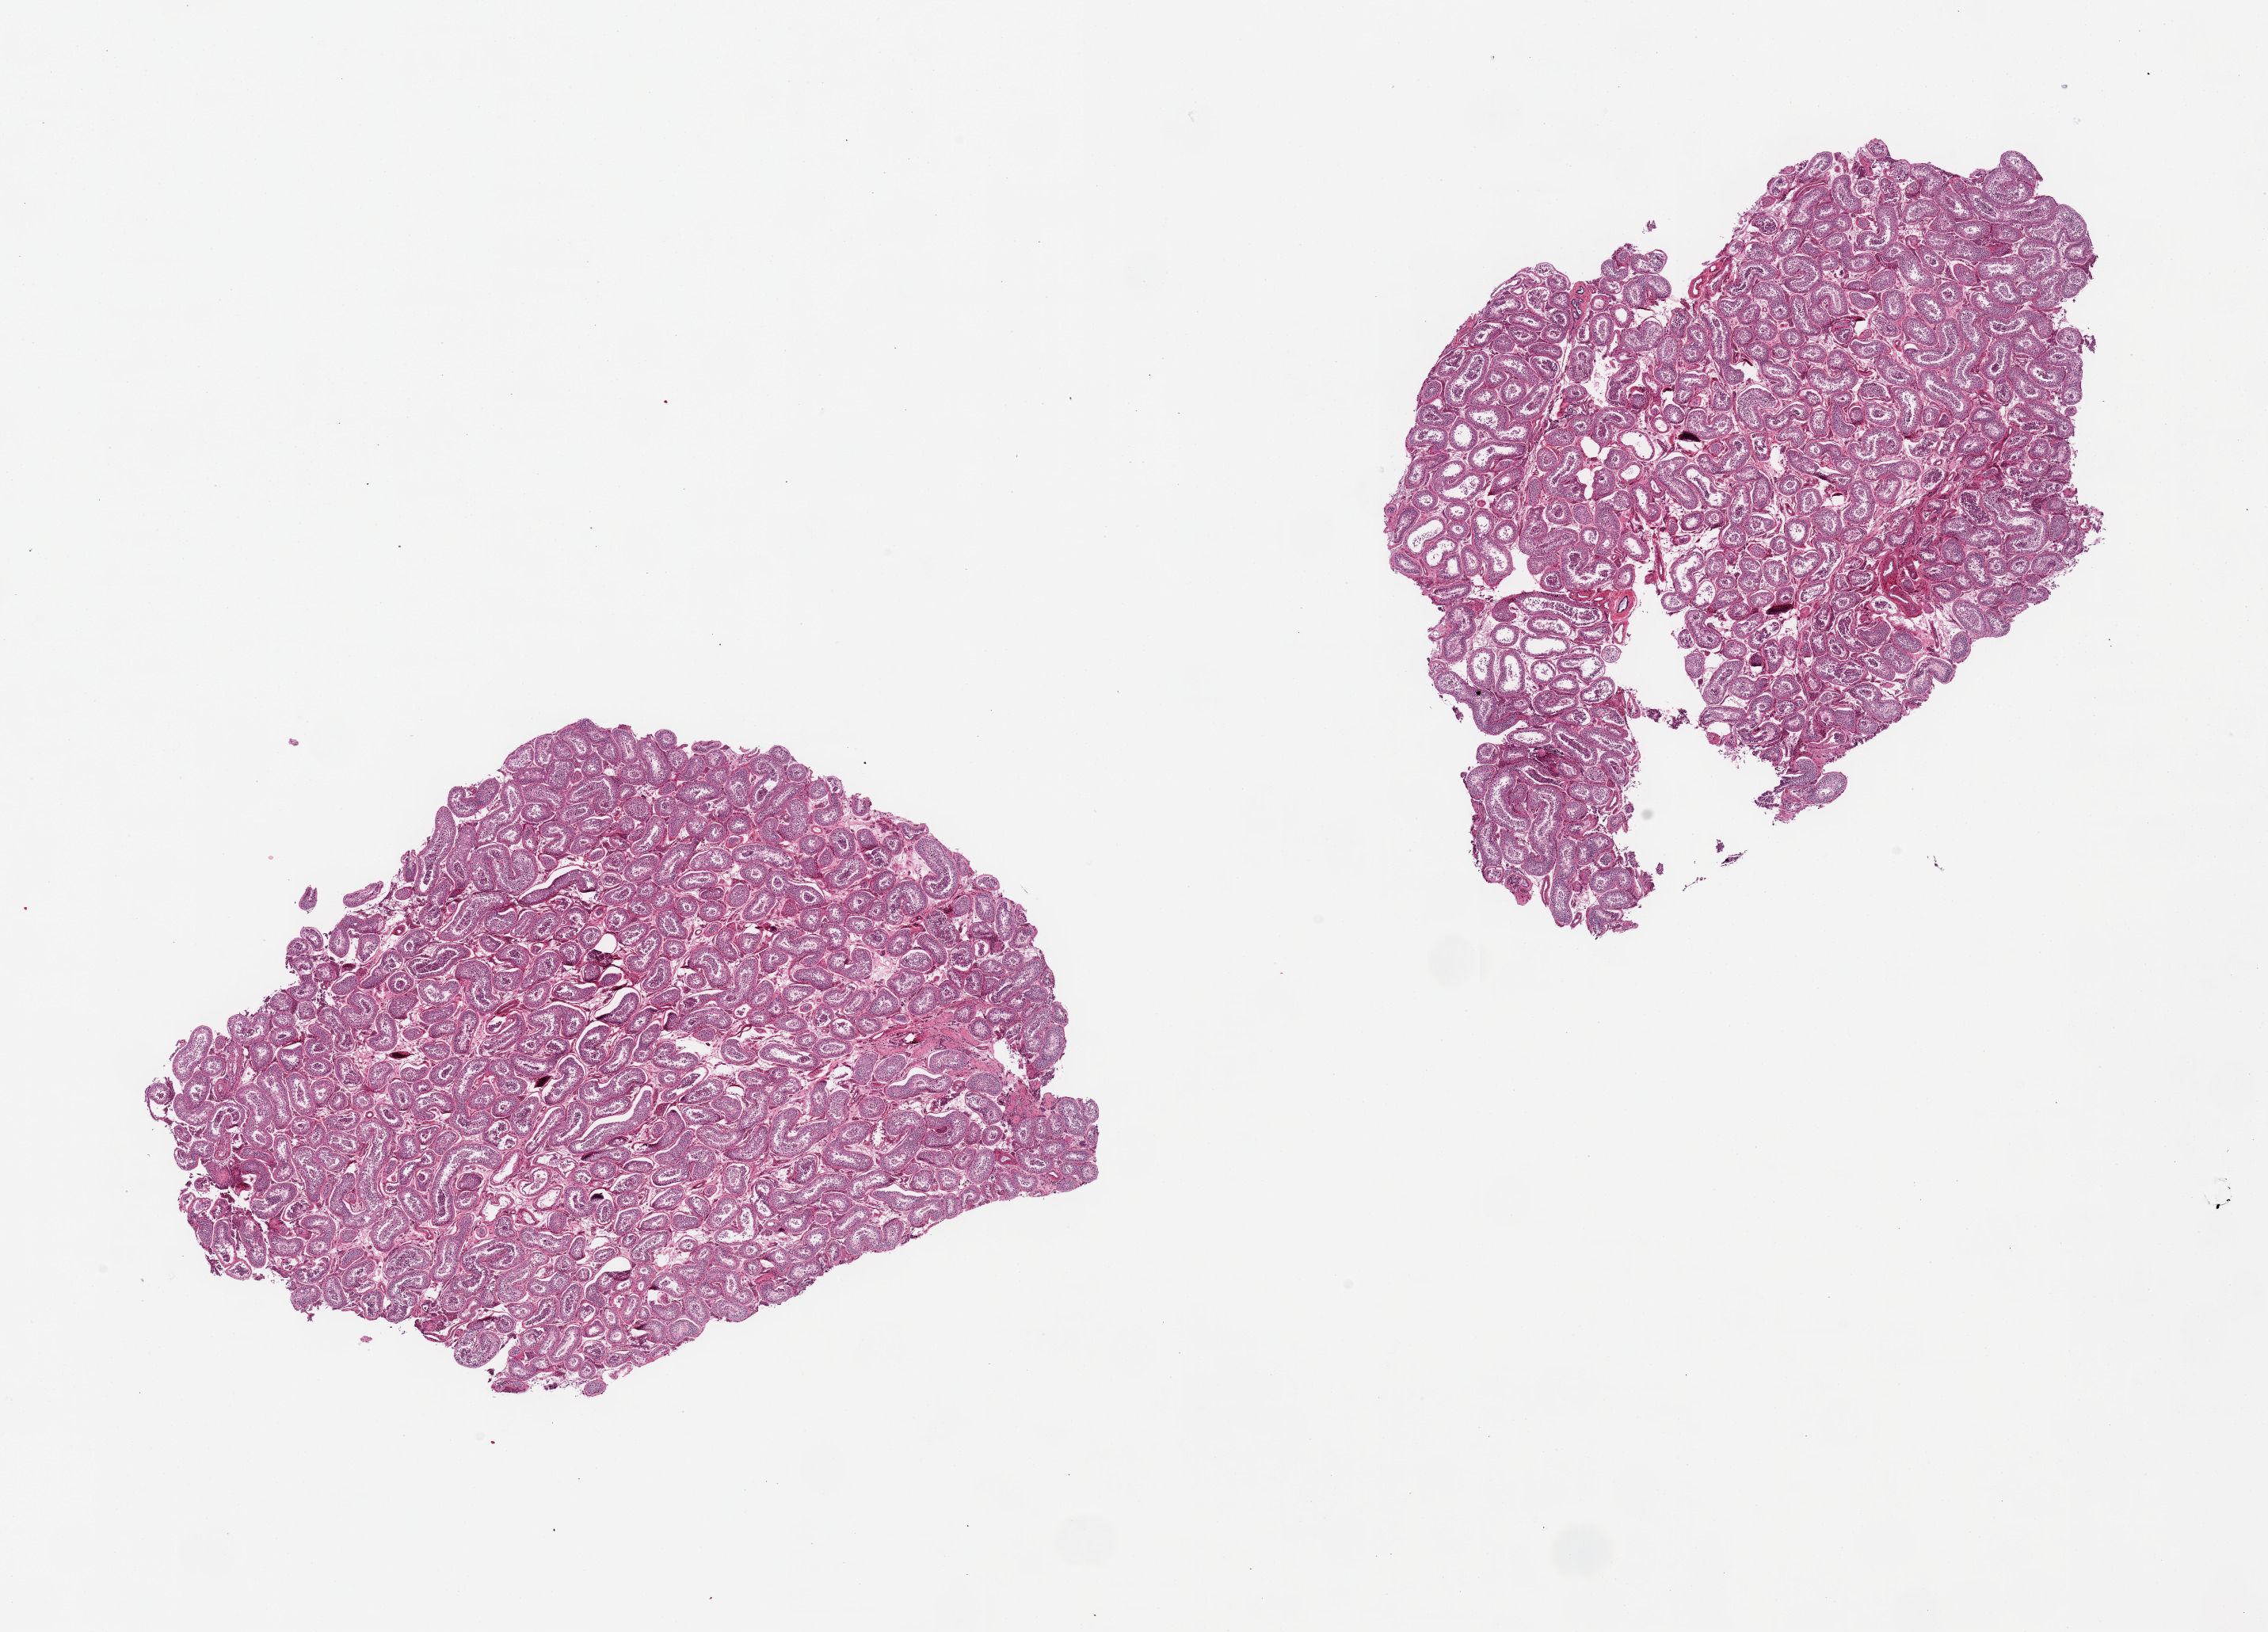
Whole-slide image, H&E stain — whole scanned area (about 22.6 x 16.3 mm, from a 20x scan) shown as a low-resolution overview. PAXgene-fixed paraffin-embedded (PFPE) section. Sampled site (target tissue): testis. Donor tissue sample. Male donor.
Pathologist's review note for this sample: 2 pieces; spermatogenesis present.